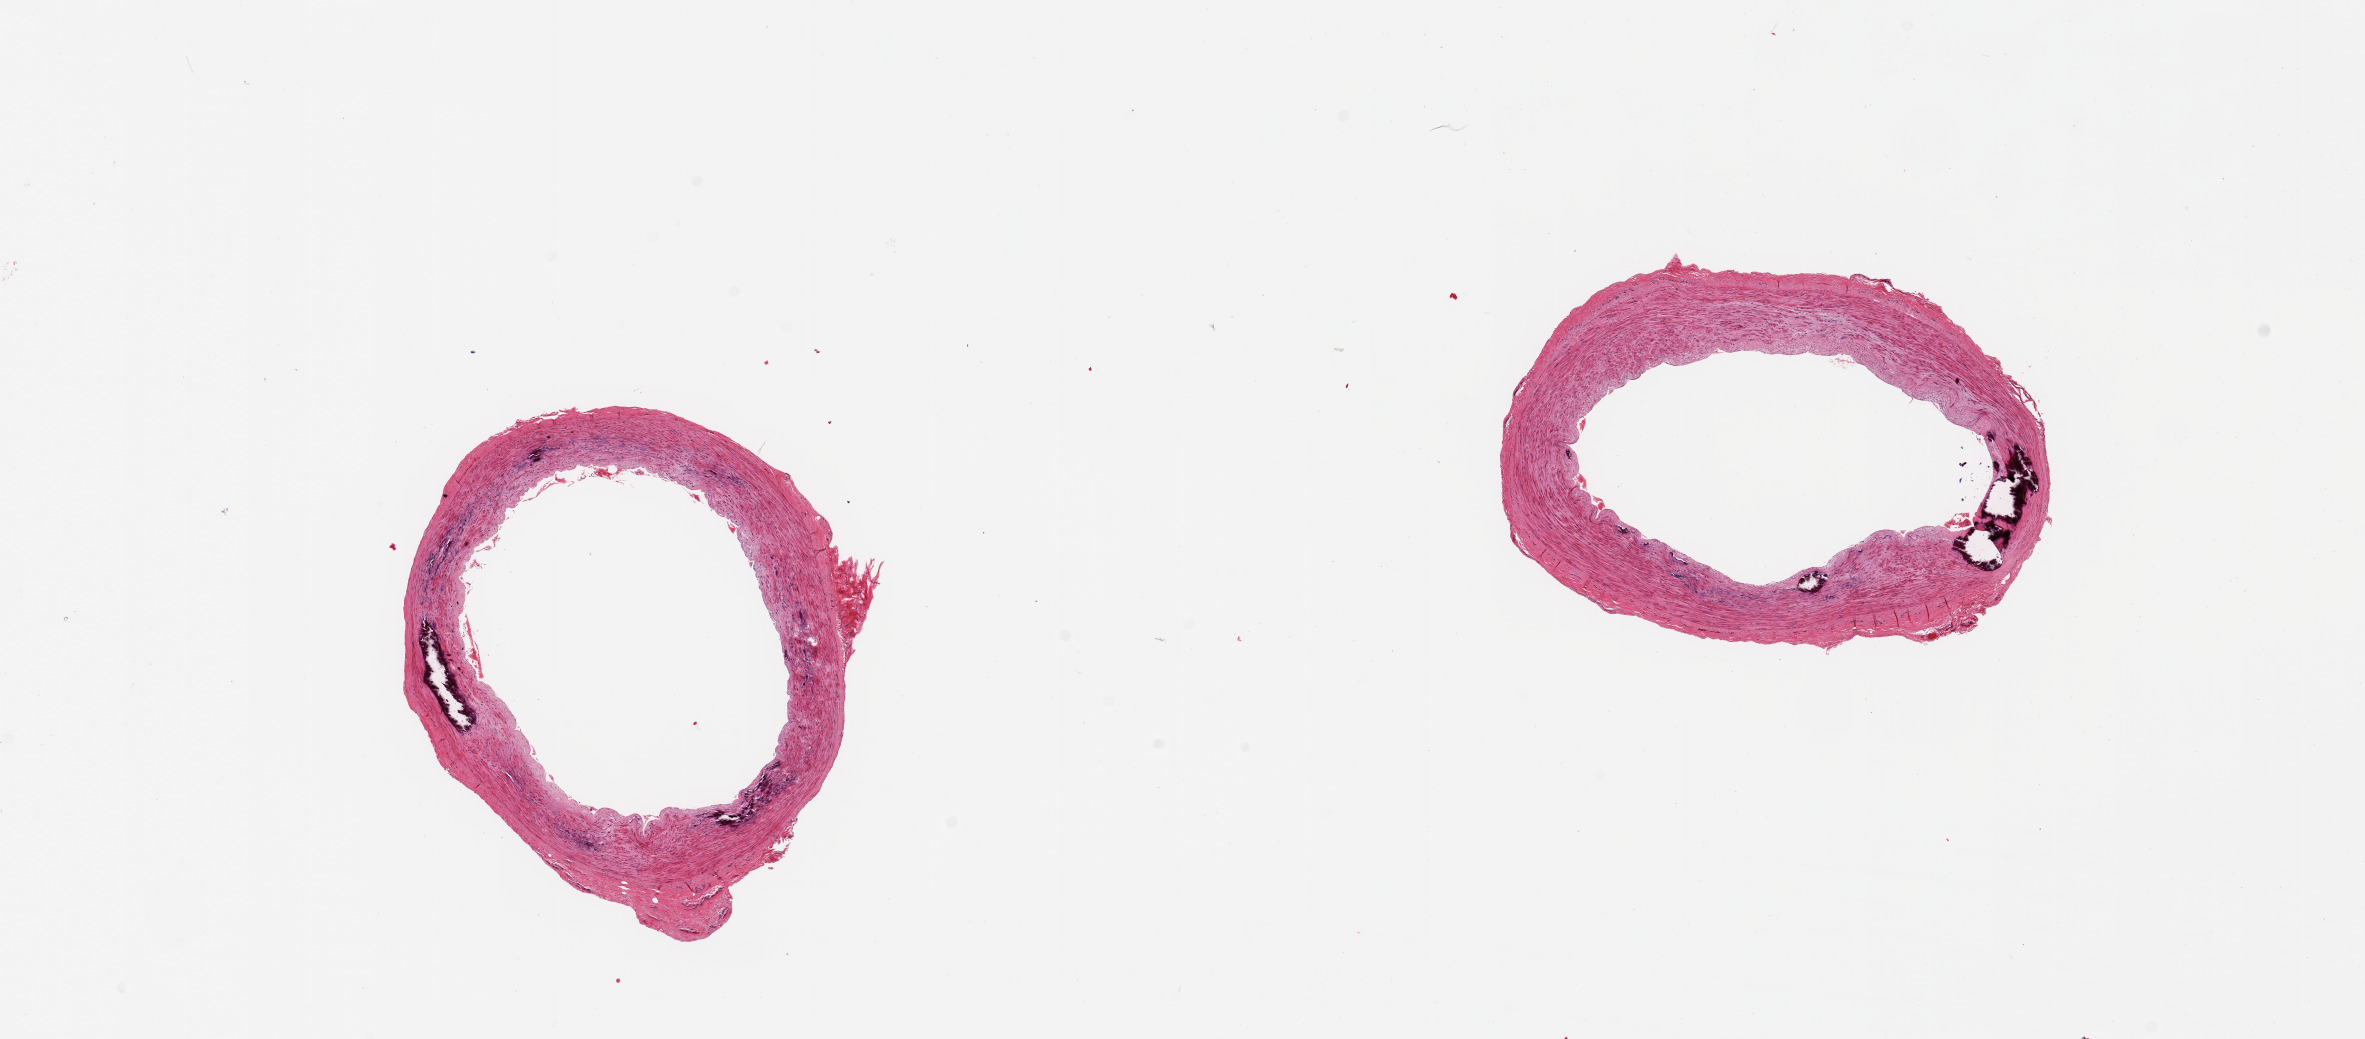
Whole-slide image, hematoxylin and eosin (H&E) stain, brightfield, a low-resolution overview of the entire scanned area, about 18.7 x 8.2 mm (from a 20x scan), PAXgene-fixed paraffin-embedded (PFPE) section, sampled site (target tissue): tibial artery, donor tissue sample. Male donor.
Review note (as recorded): 2 pieces, minimal atherosis, no adherent fat; Monckeberg medial sclerosis.